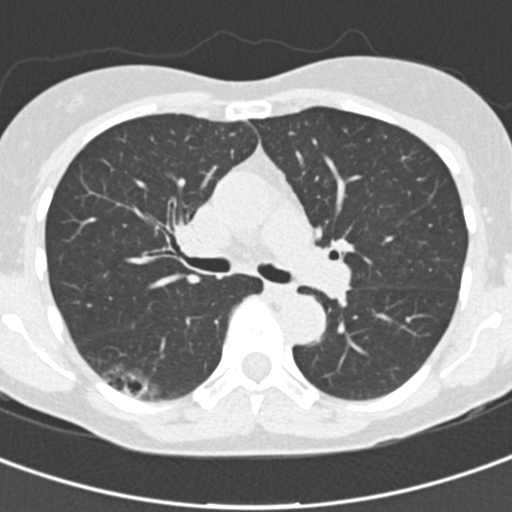
Axial slice from a low-dose chest CT screening exam; first (baseline) screen; lung window (W 1500 / L -600 HU); 2 mm slice thickness; standard (soft-tissue) reconstruction kernel (B30f); 120 kVp; slice 67 of 162 in the series. Female, age 64 years at enrolment. Current smoker at enrolment.
Lesion marked by an expert reader, box from (x=82, y=348) to (x=174, y=414) px. Screening reader's record for this exam (one nodule recorded; not confirmed to be the boxed lesion): non-calcified nodule or mass ≥4 mm, right lower lobe, 31 × 15 mm, poorly defined margins, ground glass attenuation. Official screen result: positive, change unspecified: nodule(s) >= 4 mm or enlarging nodule(s), mass(es), or other non-specific abnormalities suspicious for lung cancer. Lung cancer was diagnosed 91 days after this screen: bronchiolo-alveolar carcinoma, non-mucinous, right lower lobe, well differentiated (G1), stage IA (AJCC 6th edition), 20 mm at pathology.